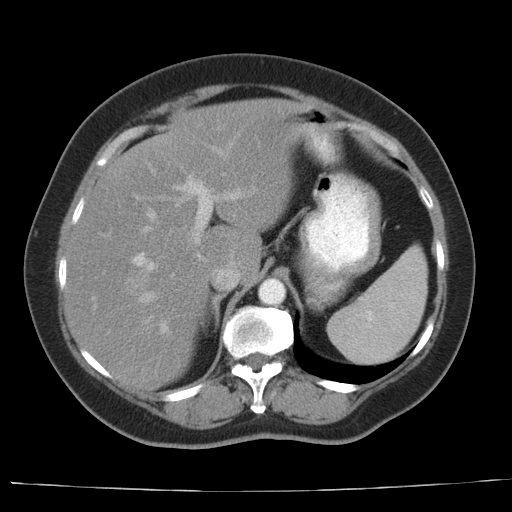
Contrast-enhanced abdominal CT, one axial slice; position 24 of 44 along the scan axis; soft-tissue window (W 400 / L 40 HU); 5 mm slice thickness; 512 × 512 image matrix. Female patient. From the clinical record (not read from this slice): diagnosis: colorectal cancer liver metastases, imaged before liver resection; multiple liver metastases: yes; largest metastasis: 1.8 cm; chemotherapy before resection: yes.
Annotated regions visible in this slice (expert manual segmentation):
- hepatic veins: bounding box [x1, y1, x2, y2] px = [141, 174, 224, 322]
- liver: [63, 99, 303, 391]
- planned liver remnant (the part of the liver to remain after resection): [99, 100, 303, 283]
- portal vein (with intrahepatic branches): [126, 123, 256, 335]